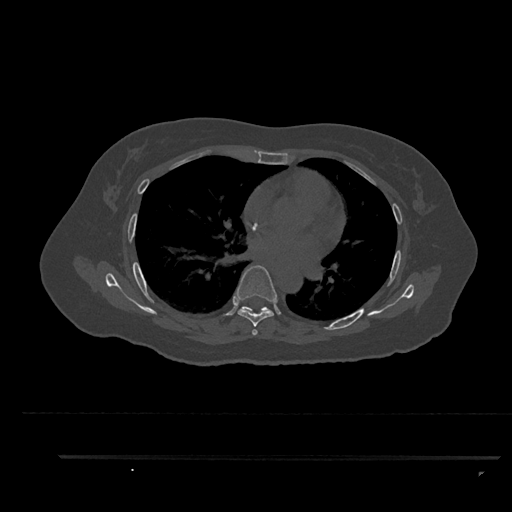
CT including the spine, one axial slice; slice 548 of 797 in the series (ordered by position); bone window (W 1800 / L 400 HU); 0.5 mm slice thickness; 512 × 512 image matrix, field of view 408 × 408 mm. Patient: female, 44 years. Case-level facts recorded for this patient, not image findings: primary cancer: renal; vertebrae with lytic lesions (as recorded): L1.
Outlined on this slice (semi-automatic segmentation, software-assisted and operator-edited):
- T6 vertebra: bounding box [x1, y1, x2, y2] px = [235, 265, 277, 335]
- T7 vertebra: [242, 306, 270, 314]